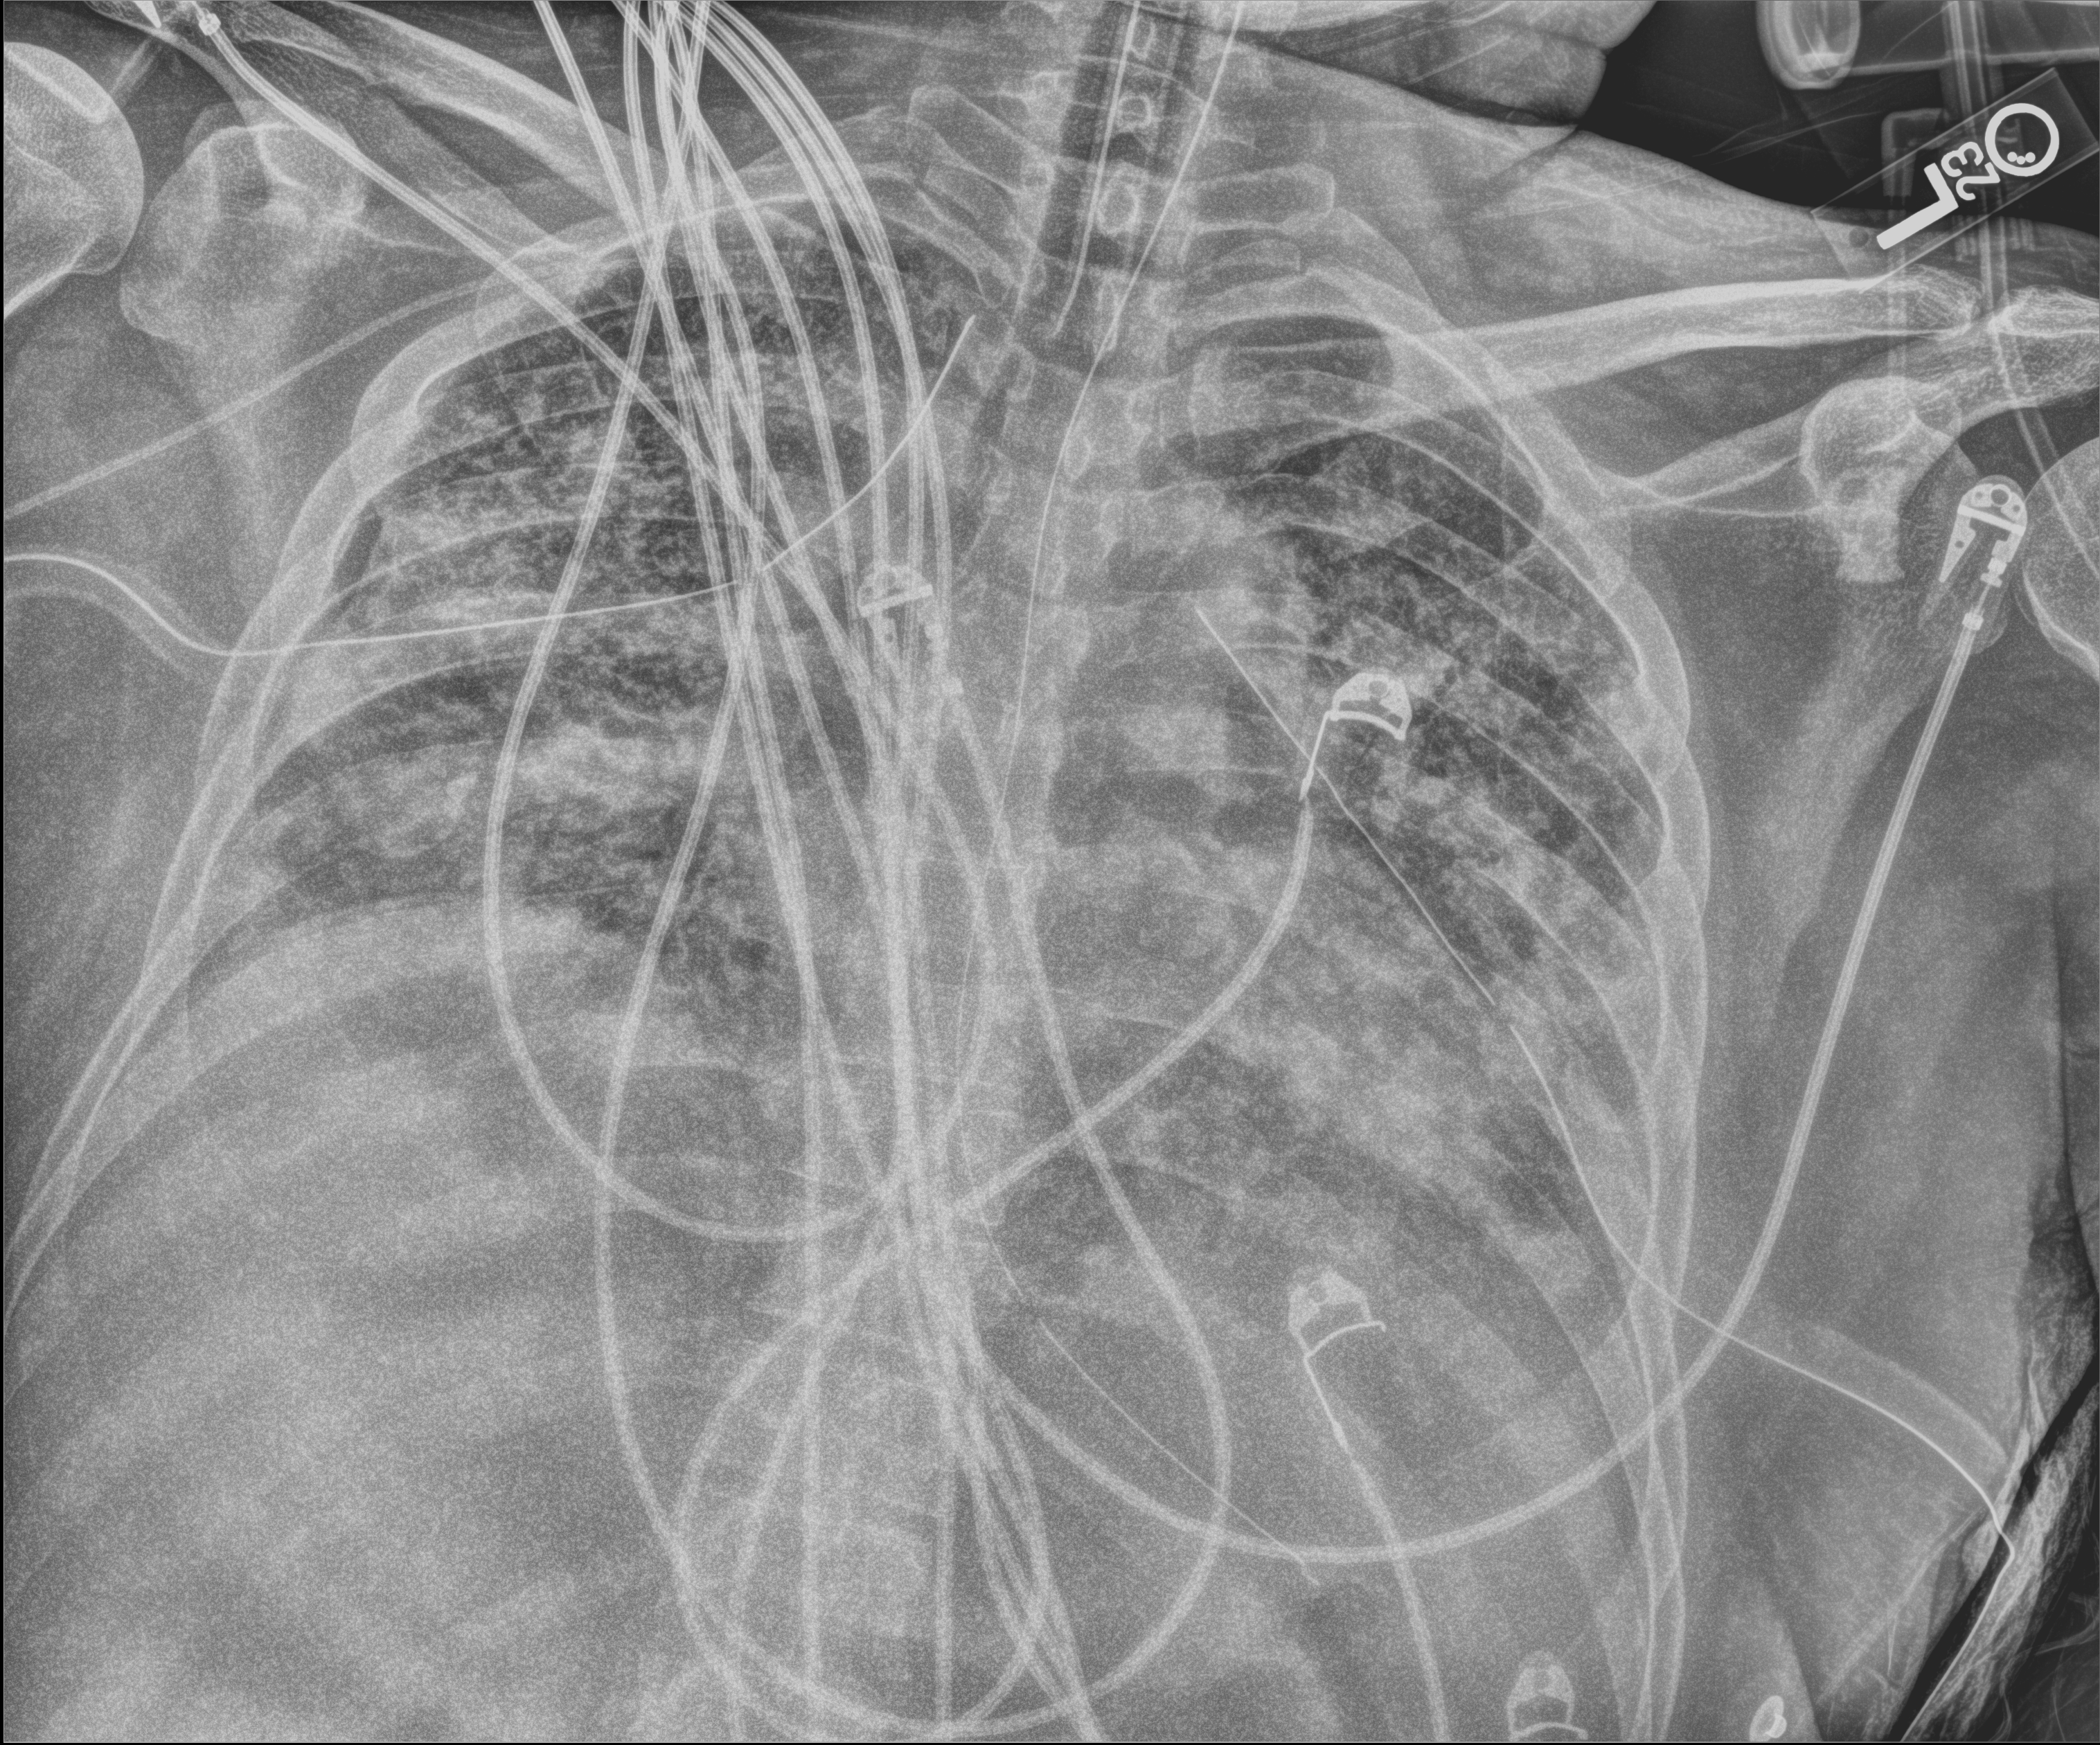
Bedside chest radiograph (digital radiography), anteroposterior (AP) projection. Male patient hospitalised with COVID-19, age 18–59 years.
Hospital-stay facts (about this admission, not read from this image; timing relative to this image not recorded): length of hospital stay: 63 days; admitted to intensive care during this hospital stay: yes.